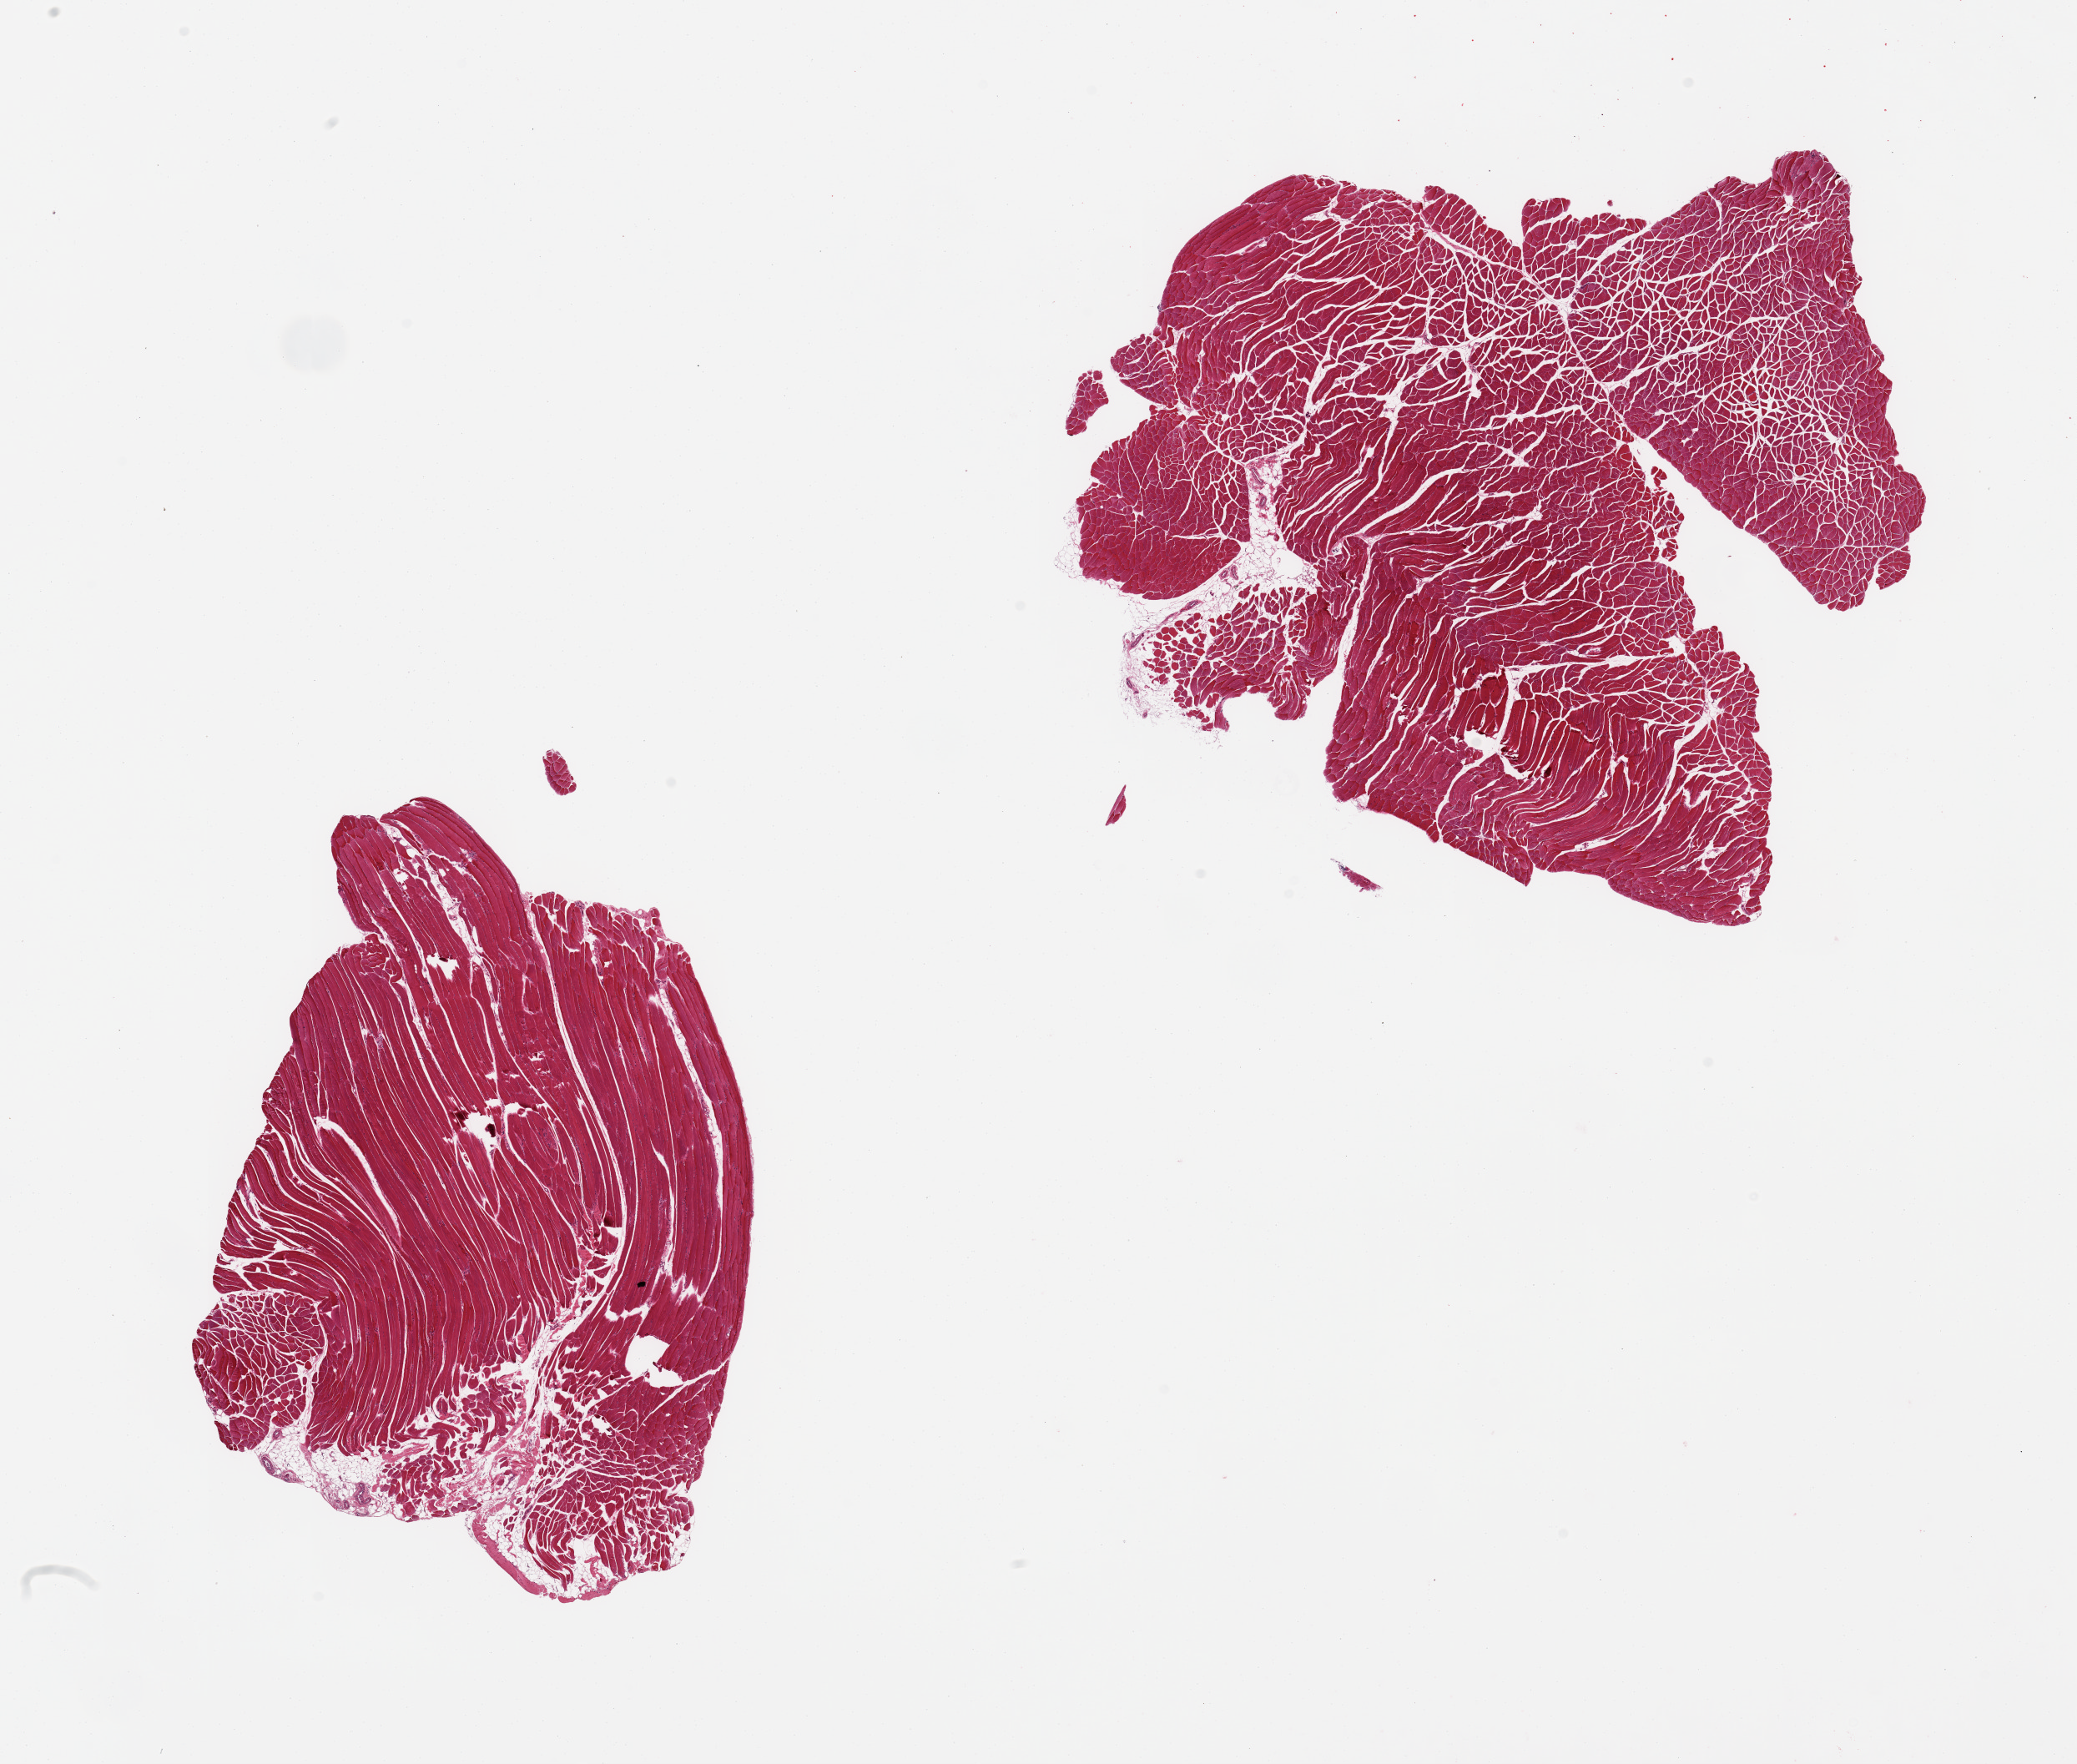
Whole-slide image, hematoxylin and eosin (H&E) stain — shown as a low-resolution overview of the whole scanned area (about 19.7 x 16.7 mm). PAXgene-fixed paraffin-embedded (PFPE) section. Section of skeletal muscle (target tissue). Tissue donor sample. Female donor.
• pathologist's review note for this sample: 2 pieces; <5% fat